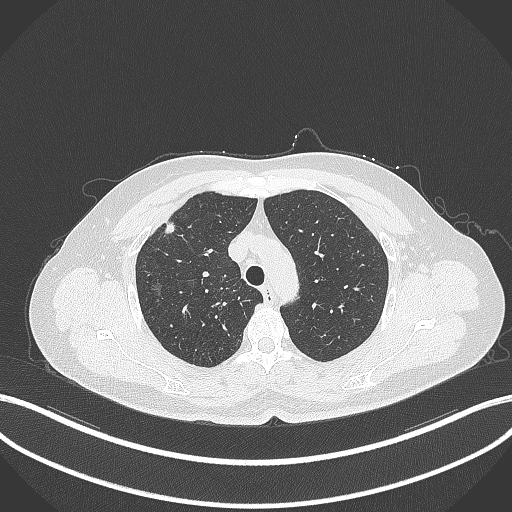
Chest CT, one axial slice. Position 282 of 353 along the scan axis. 120 kVp. Lung window (W 1500 / L -600 HU). 1 mm slice thickness. 512 × 512 image matrix, field of view 400 × 400 mm. Female patient, age 56 years. From the clinical record (not read from this slice): clinical TNM (as recorded): T1c N0 M0.
Structures marked on this image (rectangle marked by the reading radiologist):
- lung tumour (recorded histology: adenocarcinoma): box from (x=159, y=218) to (x=182, y=240) px